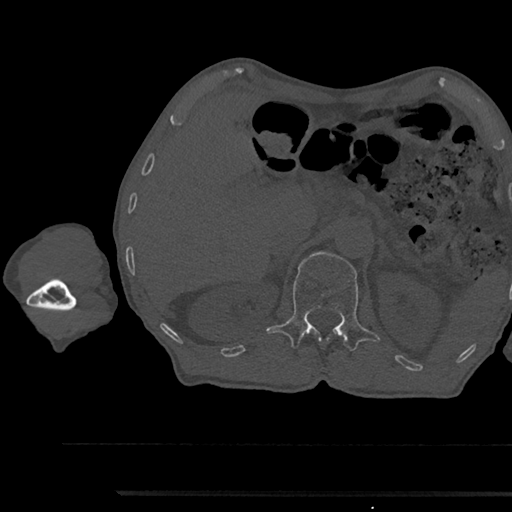
CT including the spine, one axial slice; slice 656 of 797 in the series (ordered by position); reconstruction kernel Br40s/3; 120 kVp; bone window (W 1800 / L 400 HU); 512 × 512 image matrix, field of view 367 × 367 mm. Patient: male, 79 years. From the clinical record (not read from this slice): primary cancer: prostate.
Outlined on this slice (semi-automatically segmented with operator editing):
- L1 vertebra: bounding box [x1, y1, x2, y2] px = [266, 251, 380, 351]